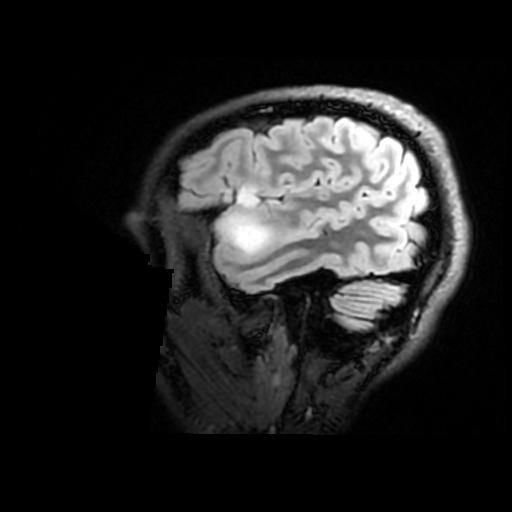
Brain MRI from a brain-tumour surgery series, one sagittal slice; slice 139 of 176 in the series (ordered by position); T2 FLAIR; 1 mm slice thickness; 512 × 512 image matrix, field of view 240 × 240 mm. Case-level facts recorded for this patient, not image findings: histopathology: Astrocytoma; WHO grade: 2; IDH mutation: yes; tumour location: Right Insular.
Outlined on this slice (manually delineated by an expert):
- tumour: bounding box [x1, y1, x2, y2] px = [224, 189, 280, 256]